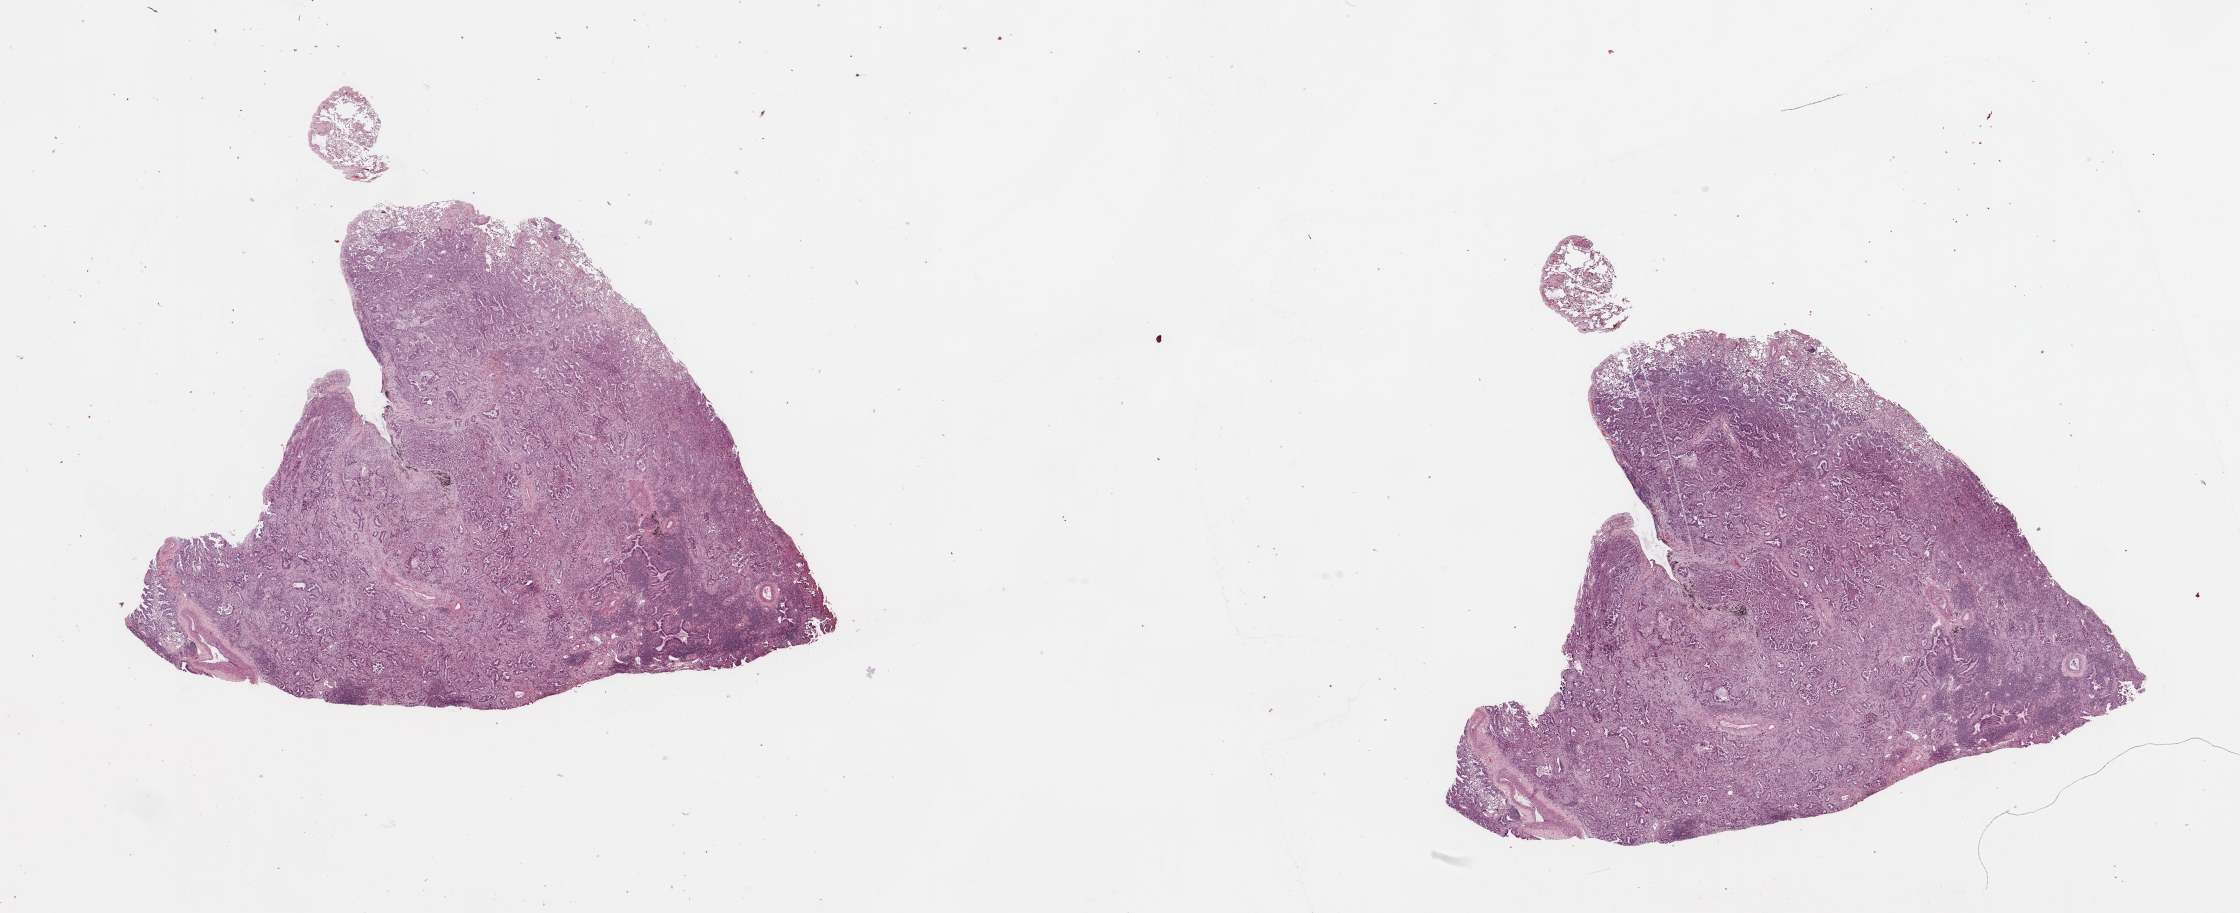
Whole-slide histology image, Hematoxylin and eosin (H&E) stained, a low-resolution overview of the entire scanned area, about 35.4 x 14.4 mm, tumour tissue sample, sampled site: lung. 67-year-old female patient. Histologic grade: G2 (moderately differentiated). Slide review estimates, as recorded: tumour nuclei 70%, necrosis 0%.
Diagnosis: Adenocarcinoma, NOS. AJCC pathologic stage: II.